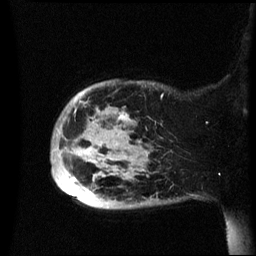
Breast MRI (dynamic contrast-enhanced), one sagittal slice. Position 9 of 60 along the scan axis. Dynamic contrast-enhanced series, image 2 of 3 at this slice position (ordered by acquisition). 1.5 T. TE 4.2 ms, TR 8.4 ms. 2.4 mm slice thickness. 256 × 256 image matrix, field of view 230 × 230 mm. Patient: female, 49 years.
Outlined on this slice (semi-automatically segmented with operator editing):
- analysis volume of interest (the breast-tissue region the enhancement analysis was run in; not a lesion): bounding box <51,80,174,209> (left, top, right, bottom; pixels)
- tumour enhancement mask (voxels above the 70 % enhancement threshold inside the analysis volume of interest): <64,114,147,200>